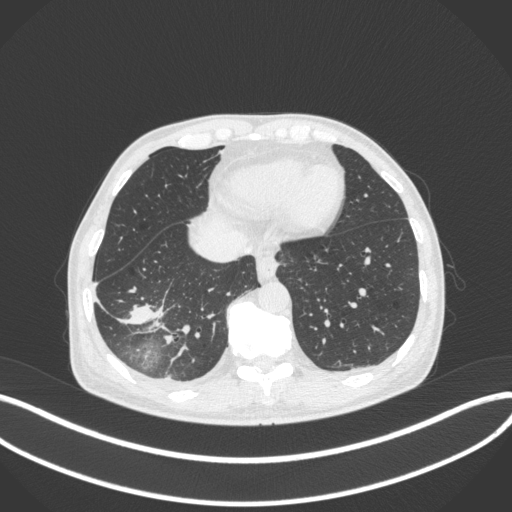
Chest CT, one axial slice; position 98 of 385 along the scan axis; lung window (W 1500 / L -600 HU); 1 mm slice thickness; 512 × 512 image matrix, field of view 400 × 400 mm. Male patient, age 64 years. Case-level facts recorded for this patient, not image findings: clinical TNM (as recorded): T3 N0 M0.
Outlined on this slice (bounding box drawn by a radiologist):
- lung tumour (recorded histology: adenocarcinoma): box from (x=115, y=288) to (x=165, y=329) px